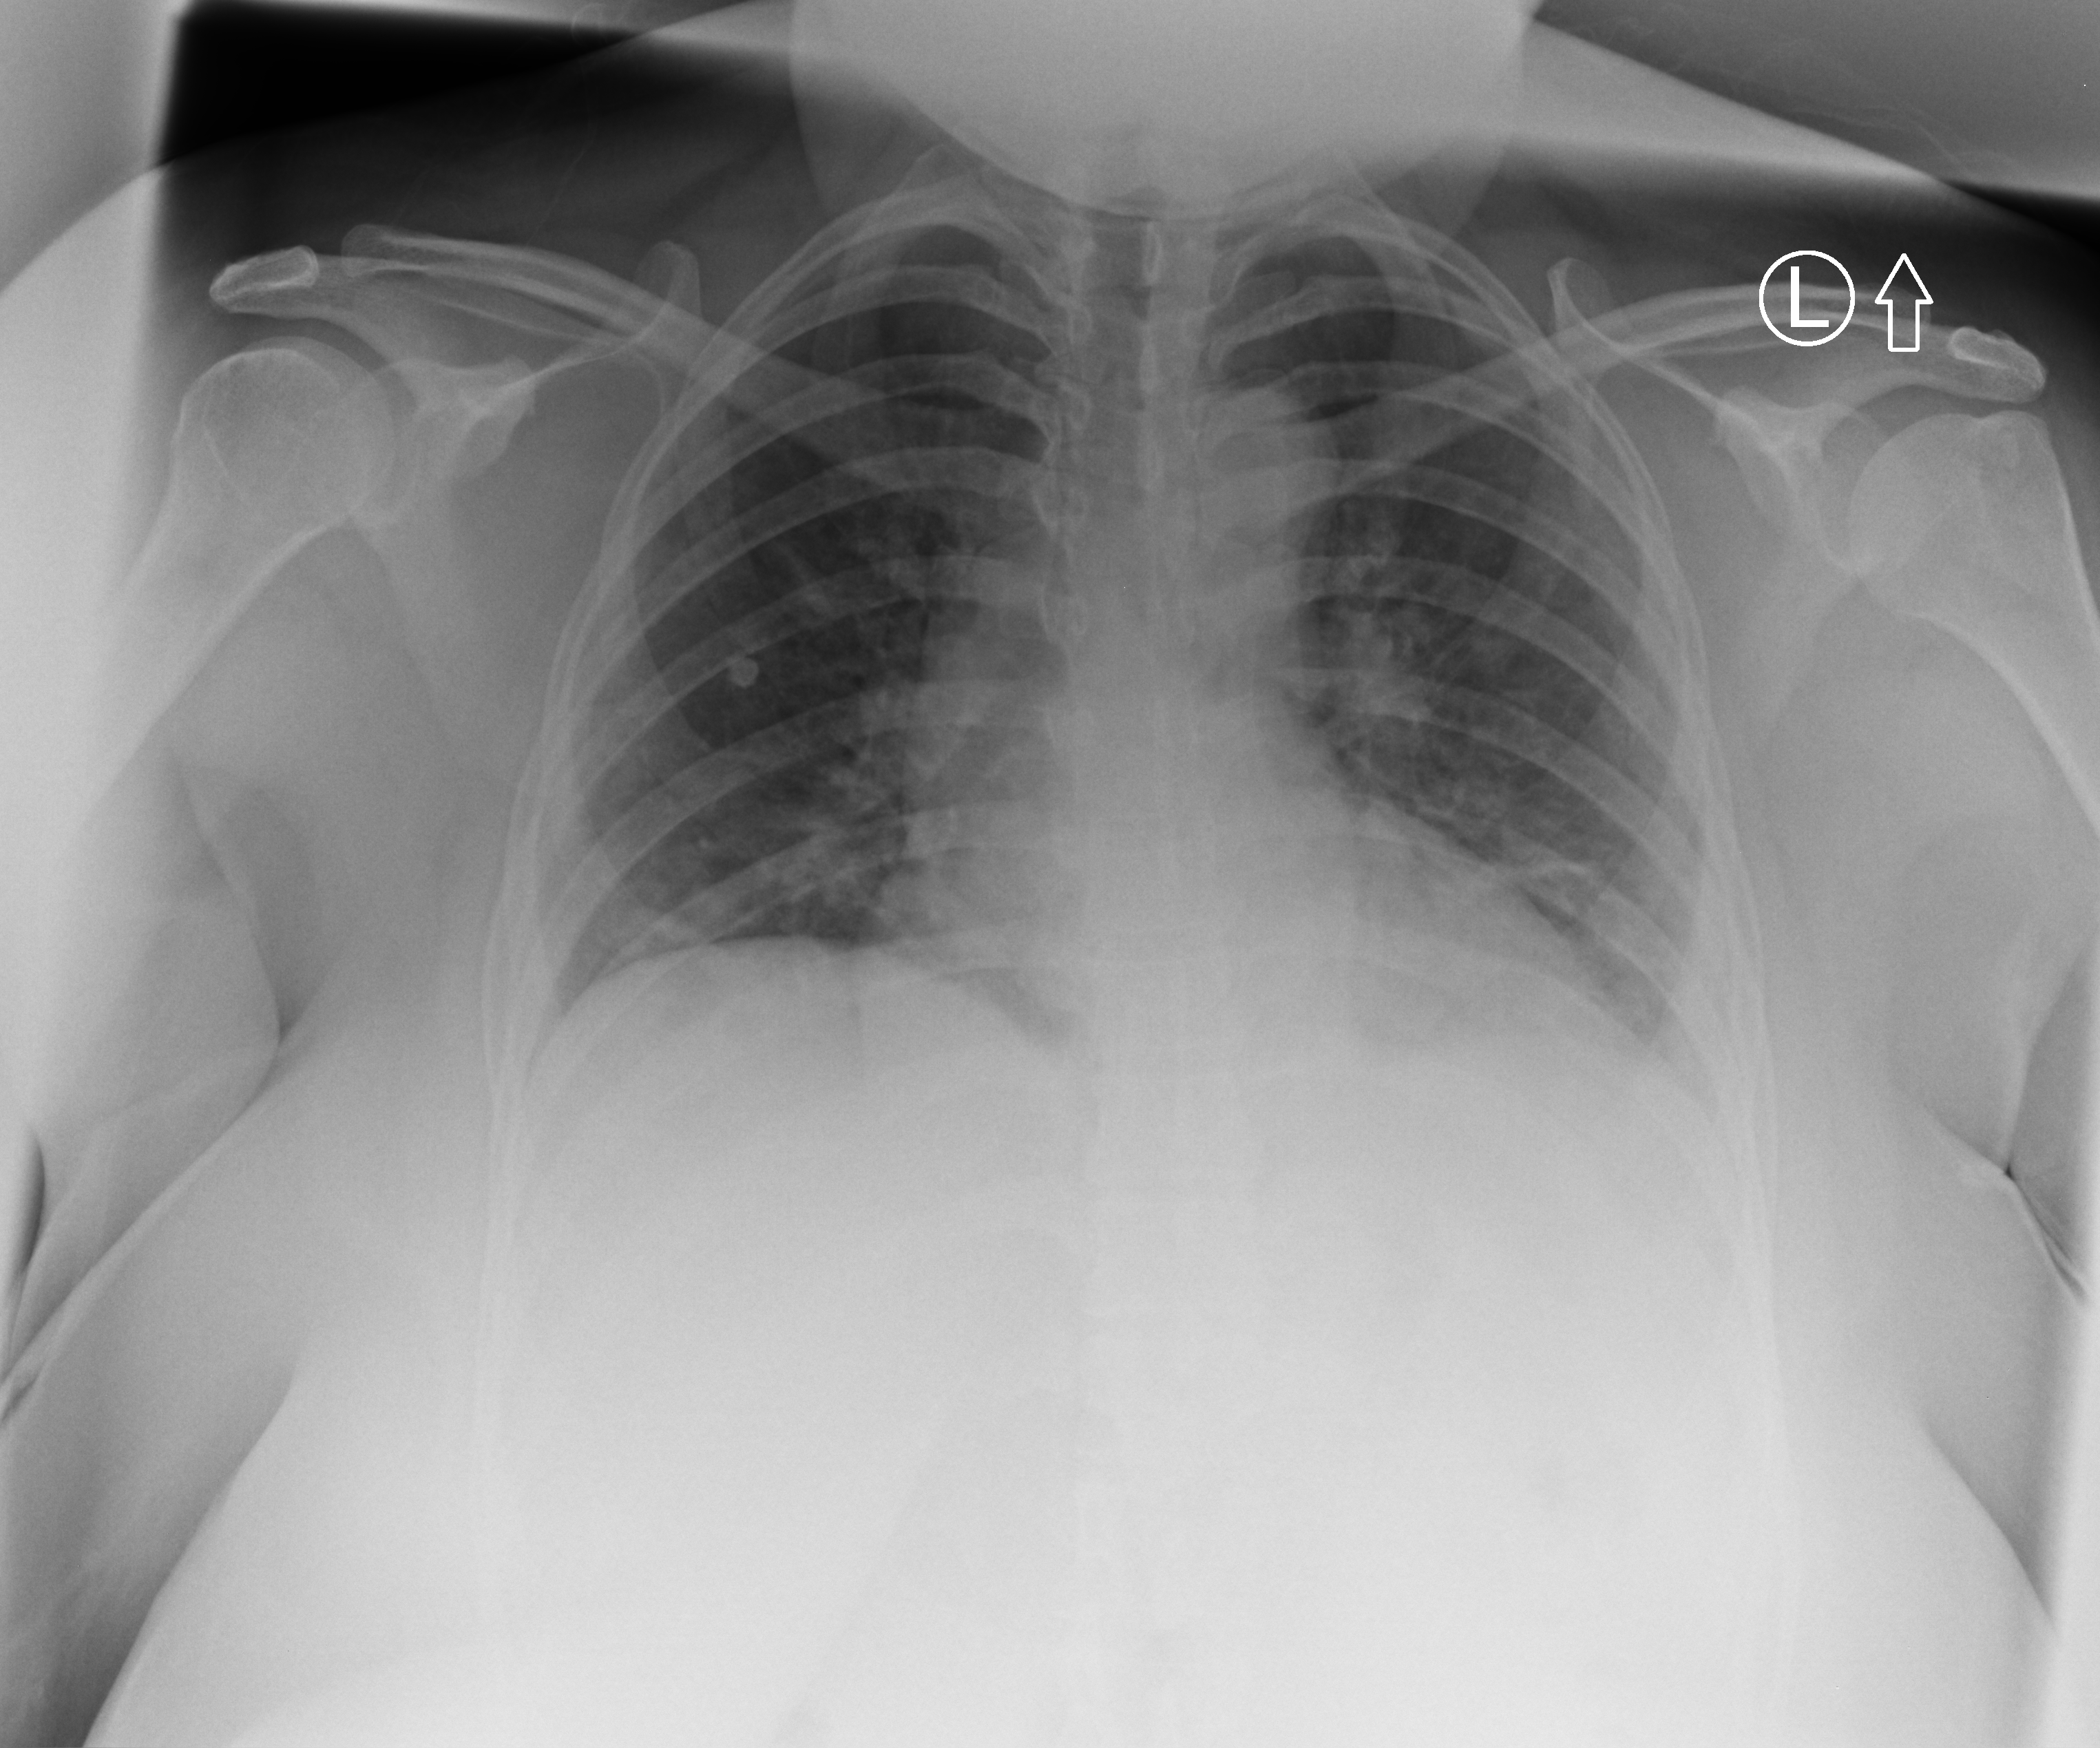
Bedside chest radiograph (computed radiography); anteroposterior (AP) projection. Female patient hospitalised with COVID-19, age 18–59 years.
Admission-level facts for this patient (not findings on this image; timing relative to this image not recorded):
- mechanically ventilated during this hospital stay: no